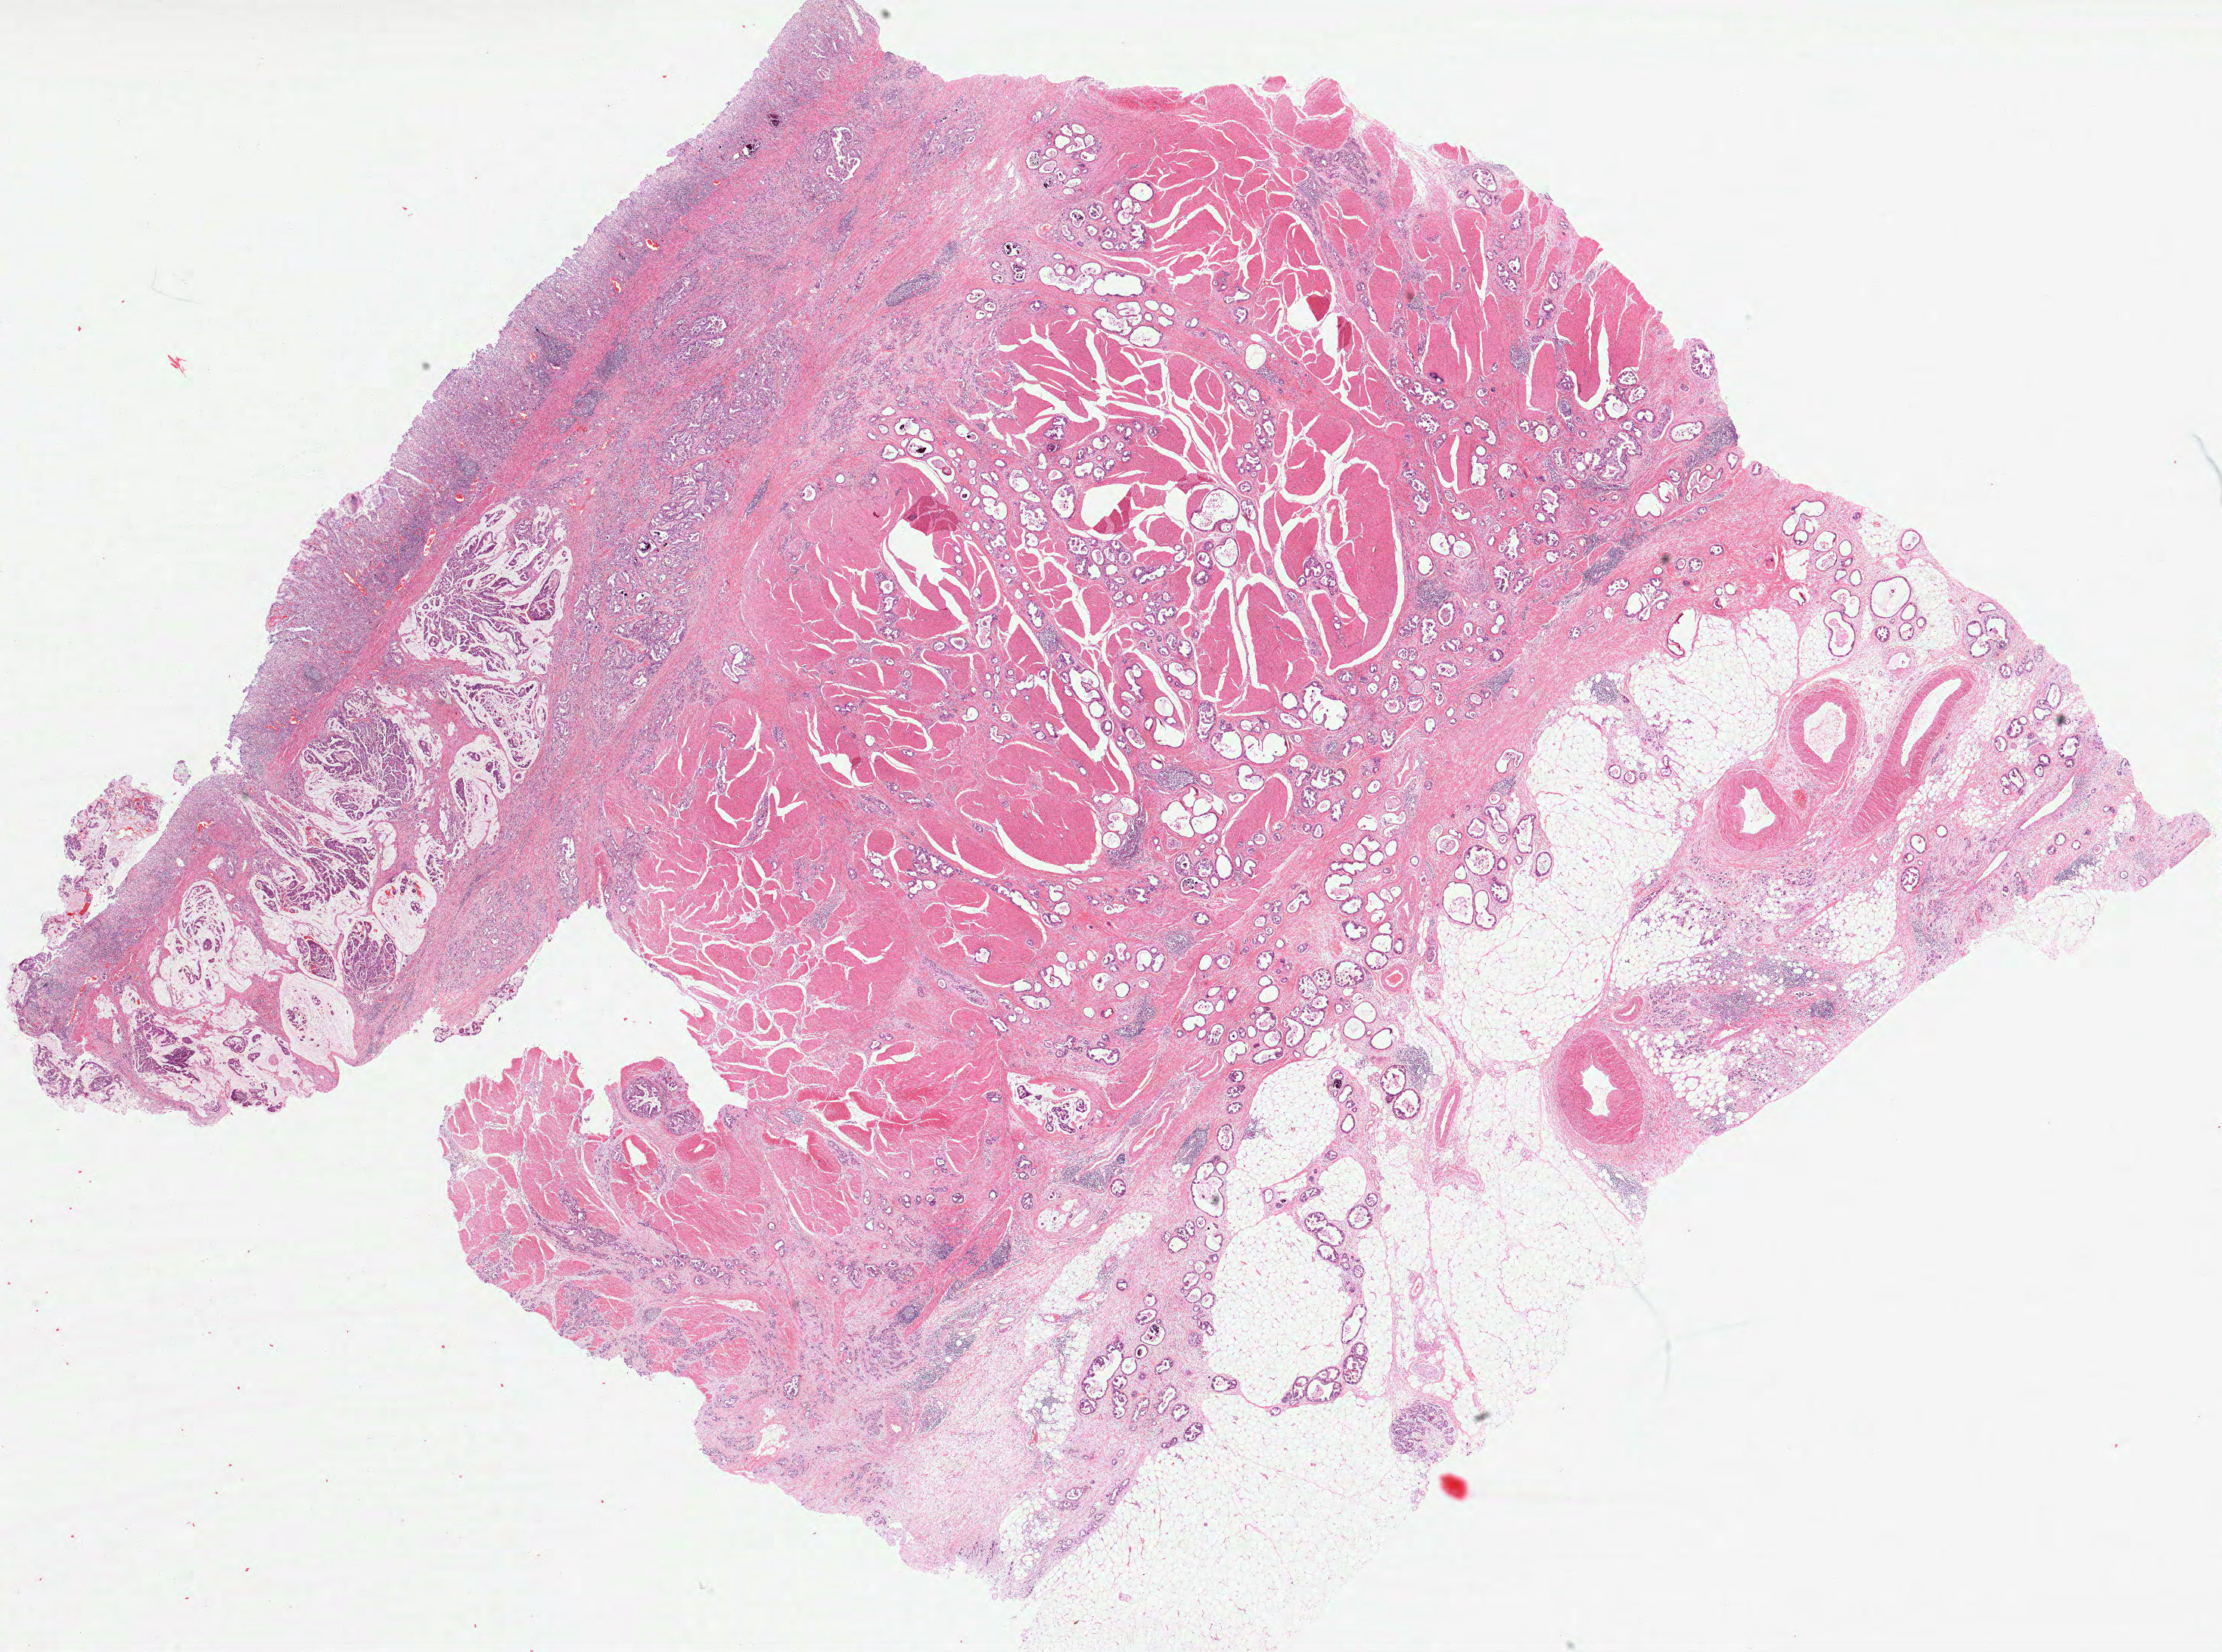
Digitized Hematoxylin and eosin (H&E) stained tissue section (whole slide) — a low-resolution overview of the entire scanned area, about 23.7 x 17.6 mm (acquisition: 40x scan), formalin-fixed paraffin-embedded (FFPE) diagnostic section, sample: primary tumour, stomach. Patient: female, age at initial diagnosis 76 years. Histologic grade: G3 (poorly differentiated).
* pathologic diagnosis: Adenocarcinoma, NOS (fundus of stomach)
* AJCC pathologic stage: IIIB (7th edition)